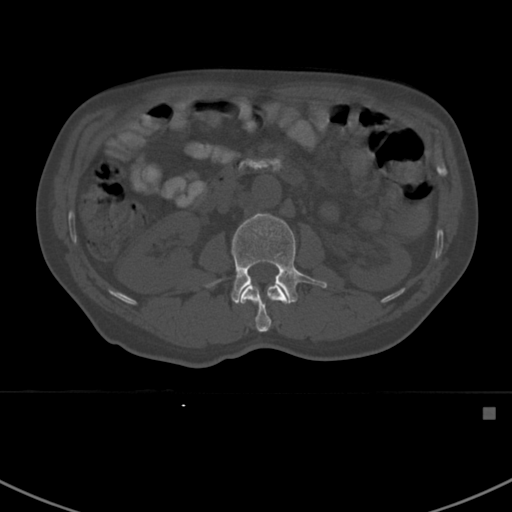
CT including the spine, one axial slice. Position 294 of 412 along the scan axis. 120 kVp. Bone window (W 1800 / L 400 HU). 1.5 mm slice thickness. 512 × 512 image matrix, field of view 358 × 358 mm. Patient: male, 59 years. Case-level facts recorded for this patient, not image findings: primary cancer: prostate.
Structures marked on this image (semi-automatically segmented with operator editing):
- L1 vertebra: bounding box <240,285,288,332> (left, top, right, bottom; pixels)
- L2 vertebra: <203,213,327,304>